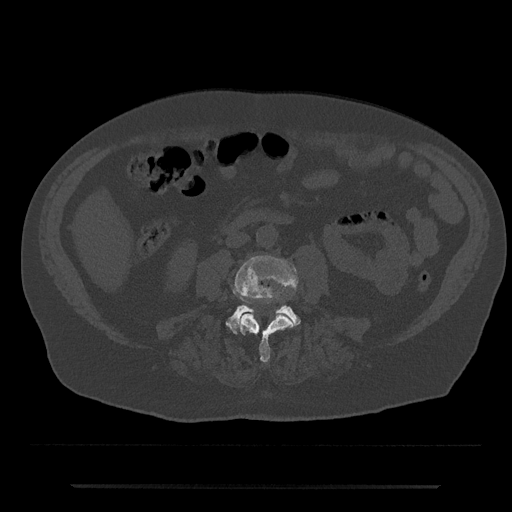
CT including the spine, one axial slice; slice 384 of 797 in the series (ordered by position); reconstruction kernel Br40s/3; 120 kVp; bone window (W 1800 / L 400 HU); 0.5 mm slice thickness; 512 × 512 image matrix, field of view 434 × 434 mm. Male patient, age 80 years. From the clinical record (not read from this slice): primary cancer: prostate; vertebrae with lytic lesions (as recorded): L1, T11.
Annotated regions visible in this slice (semi-automatic segmentation, software-assisted and operator-edited):
- L3 vertebra: box from (x=233, y=255) to (x=298, y=363) px
- L4 vertebra: (x=226, y=305)–(x=301, y=334)